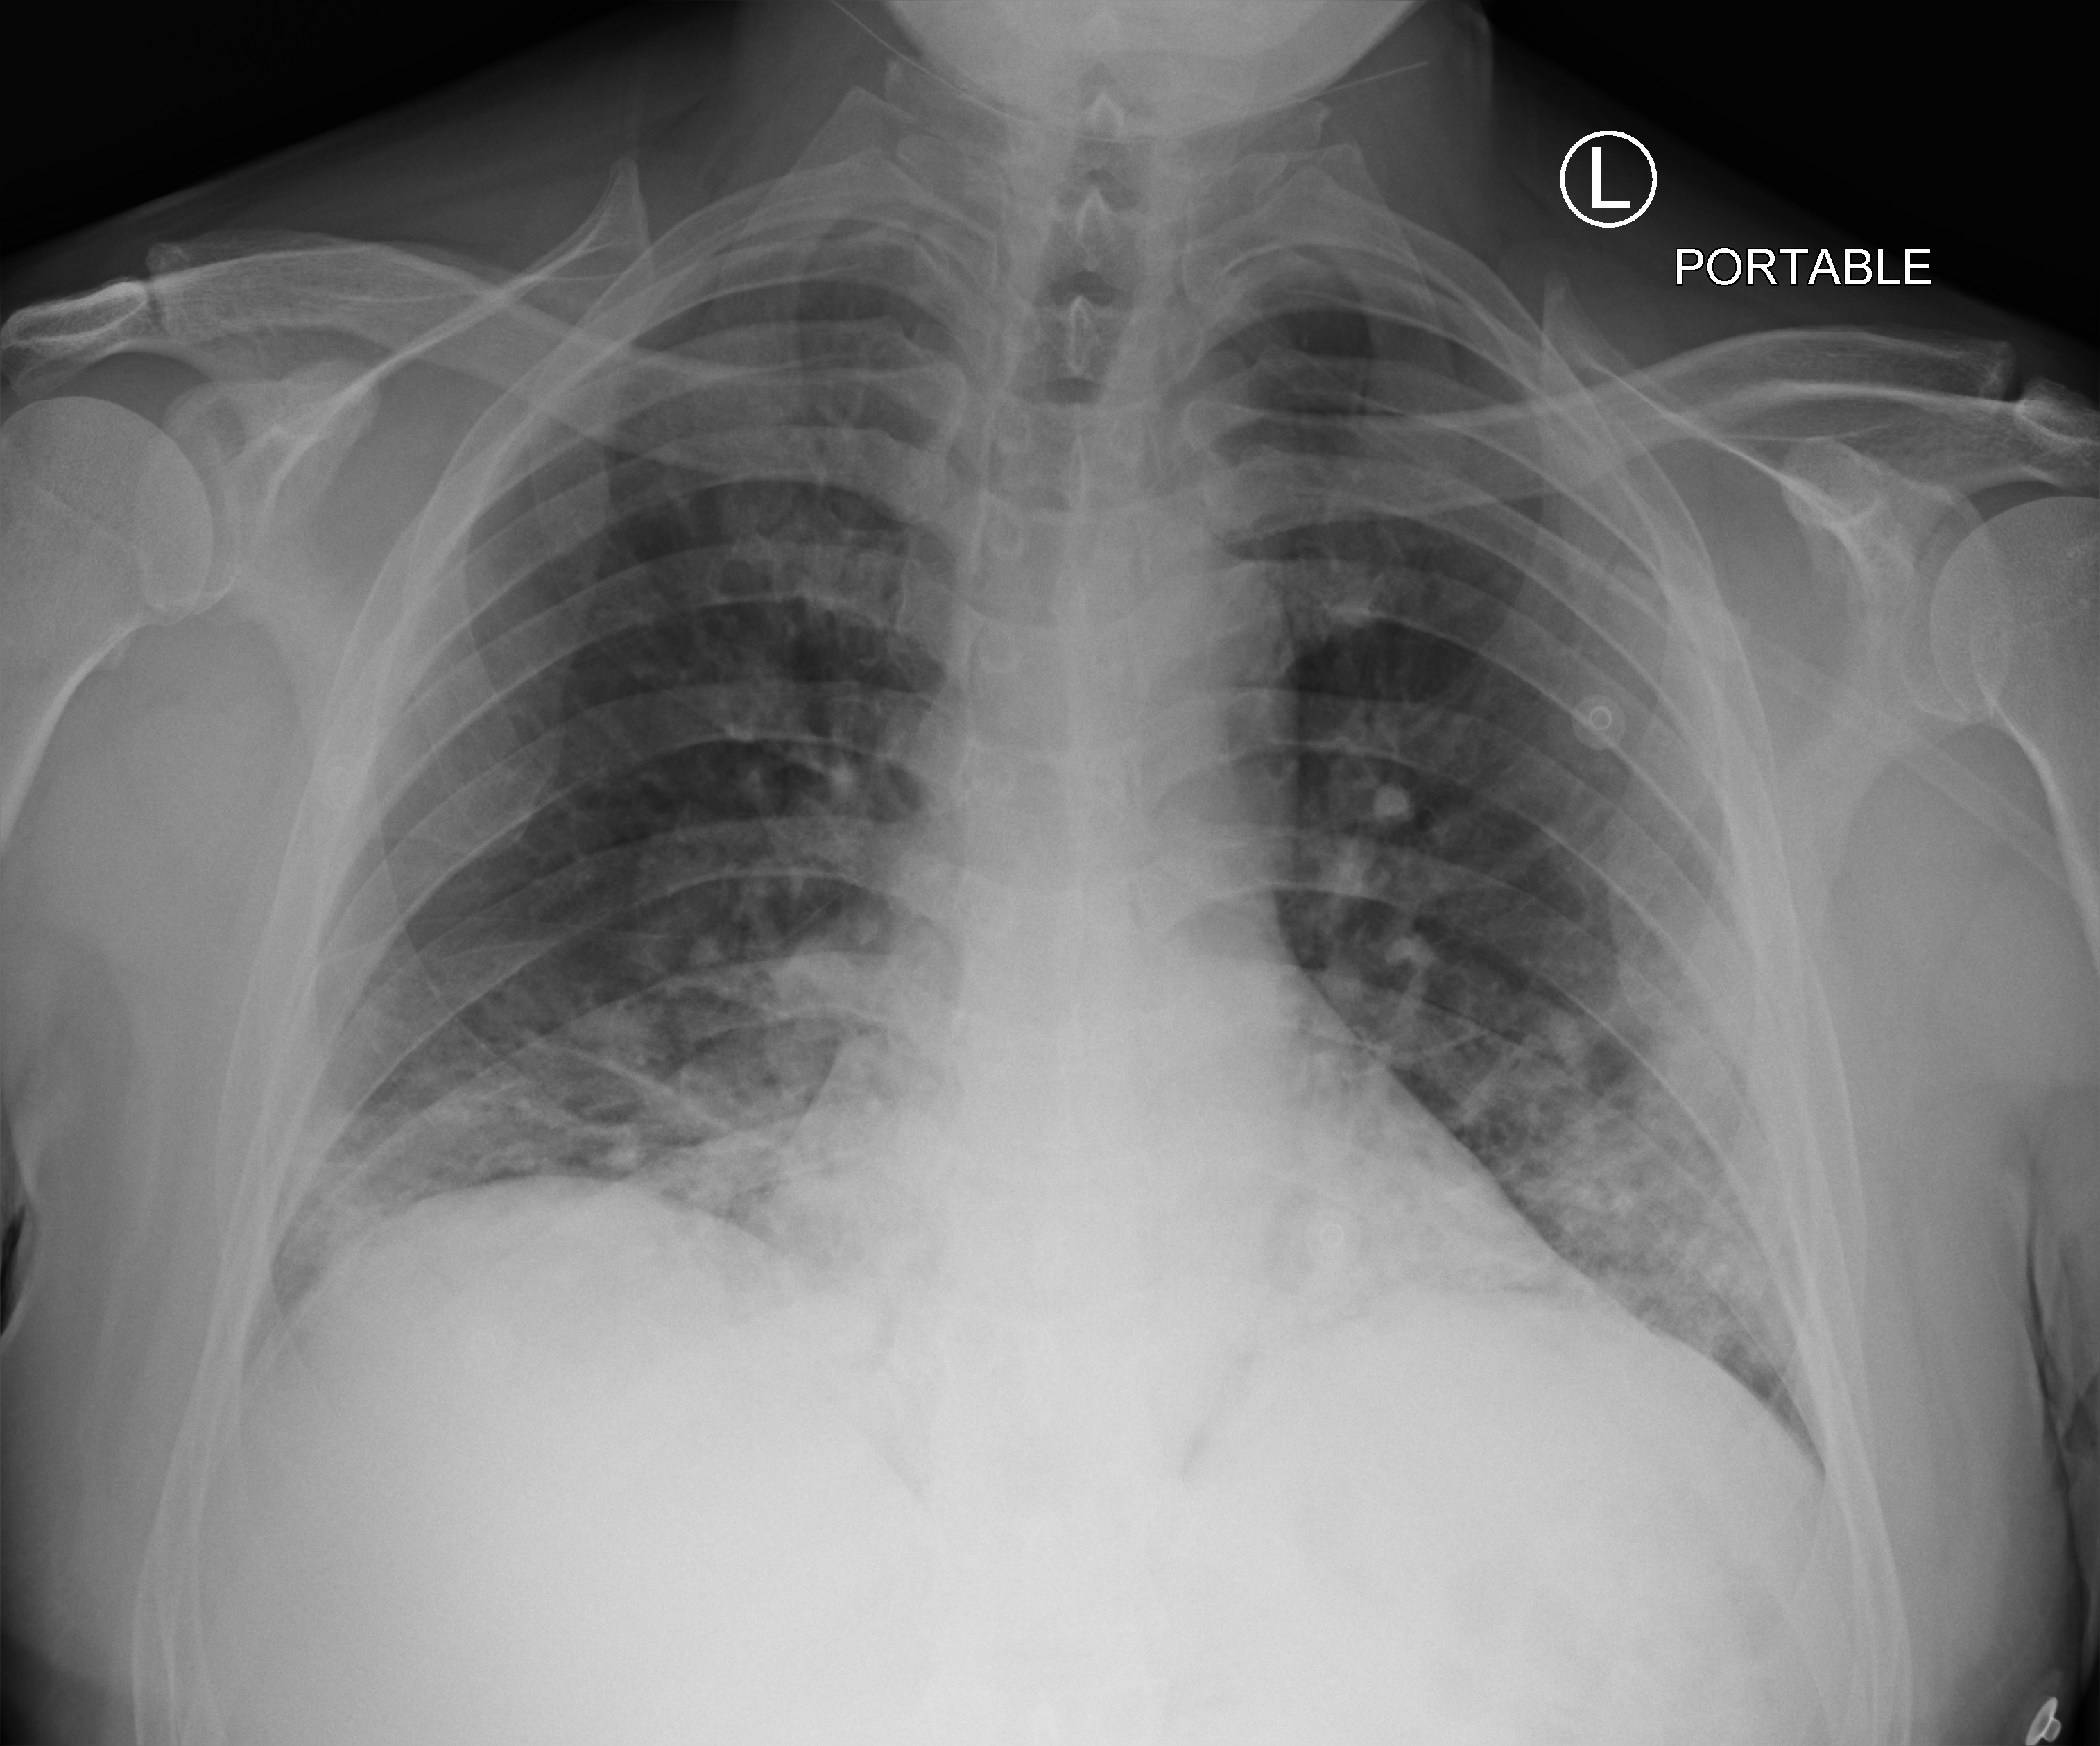
Chest X-ray (portable), anteroposterior (AP) projection. Male patient hospitalised with COVID-19, age 18–59 years.
Hospital-stay facts (about this admission, not read from this image; timing relative to this image not recorded): admitted to intensive care during this hospital stay: no; chronic kidney disease (admission record): no.